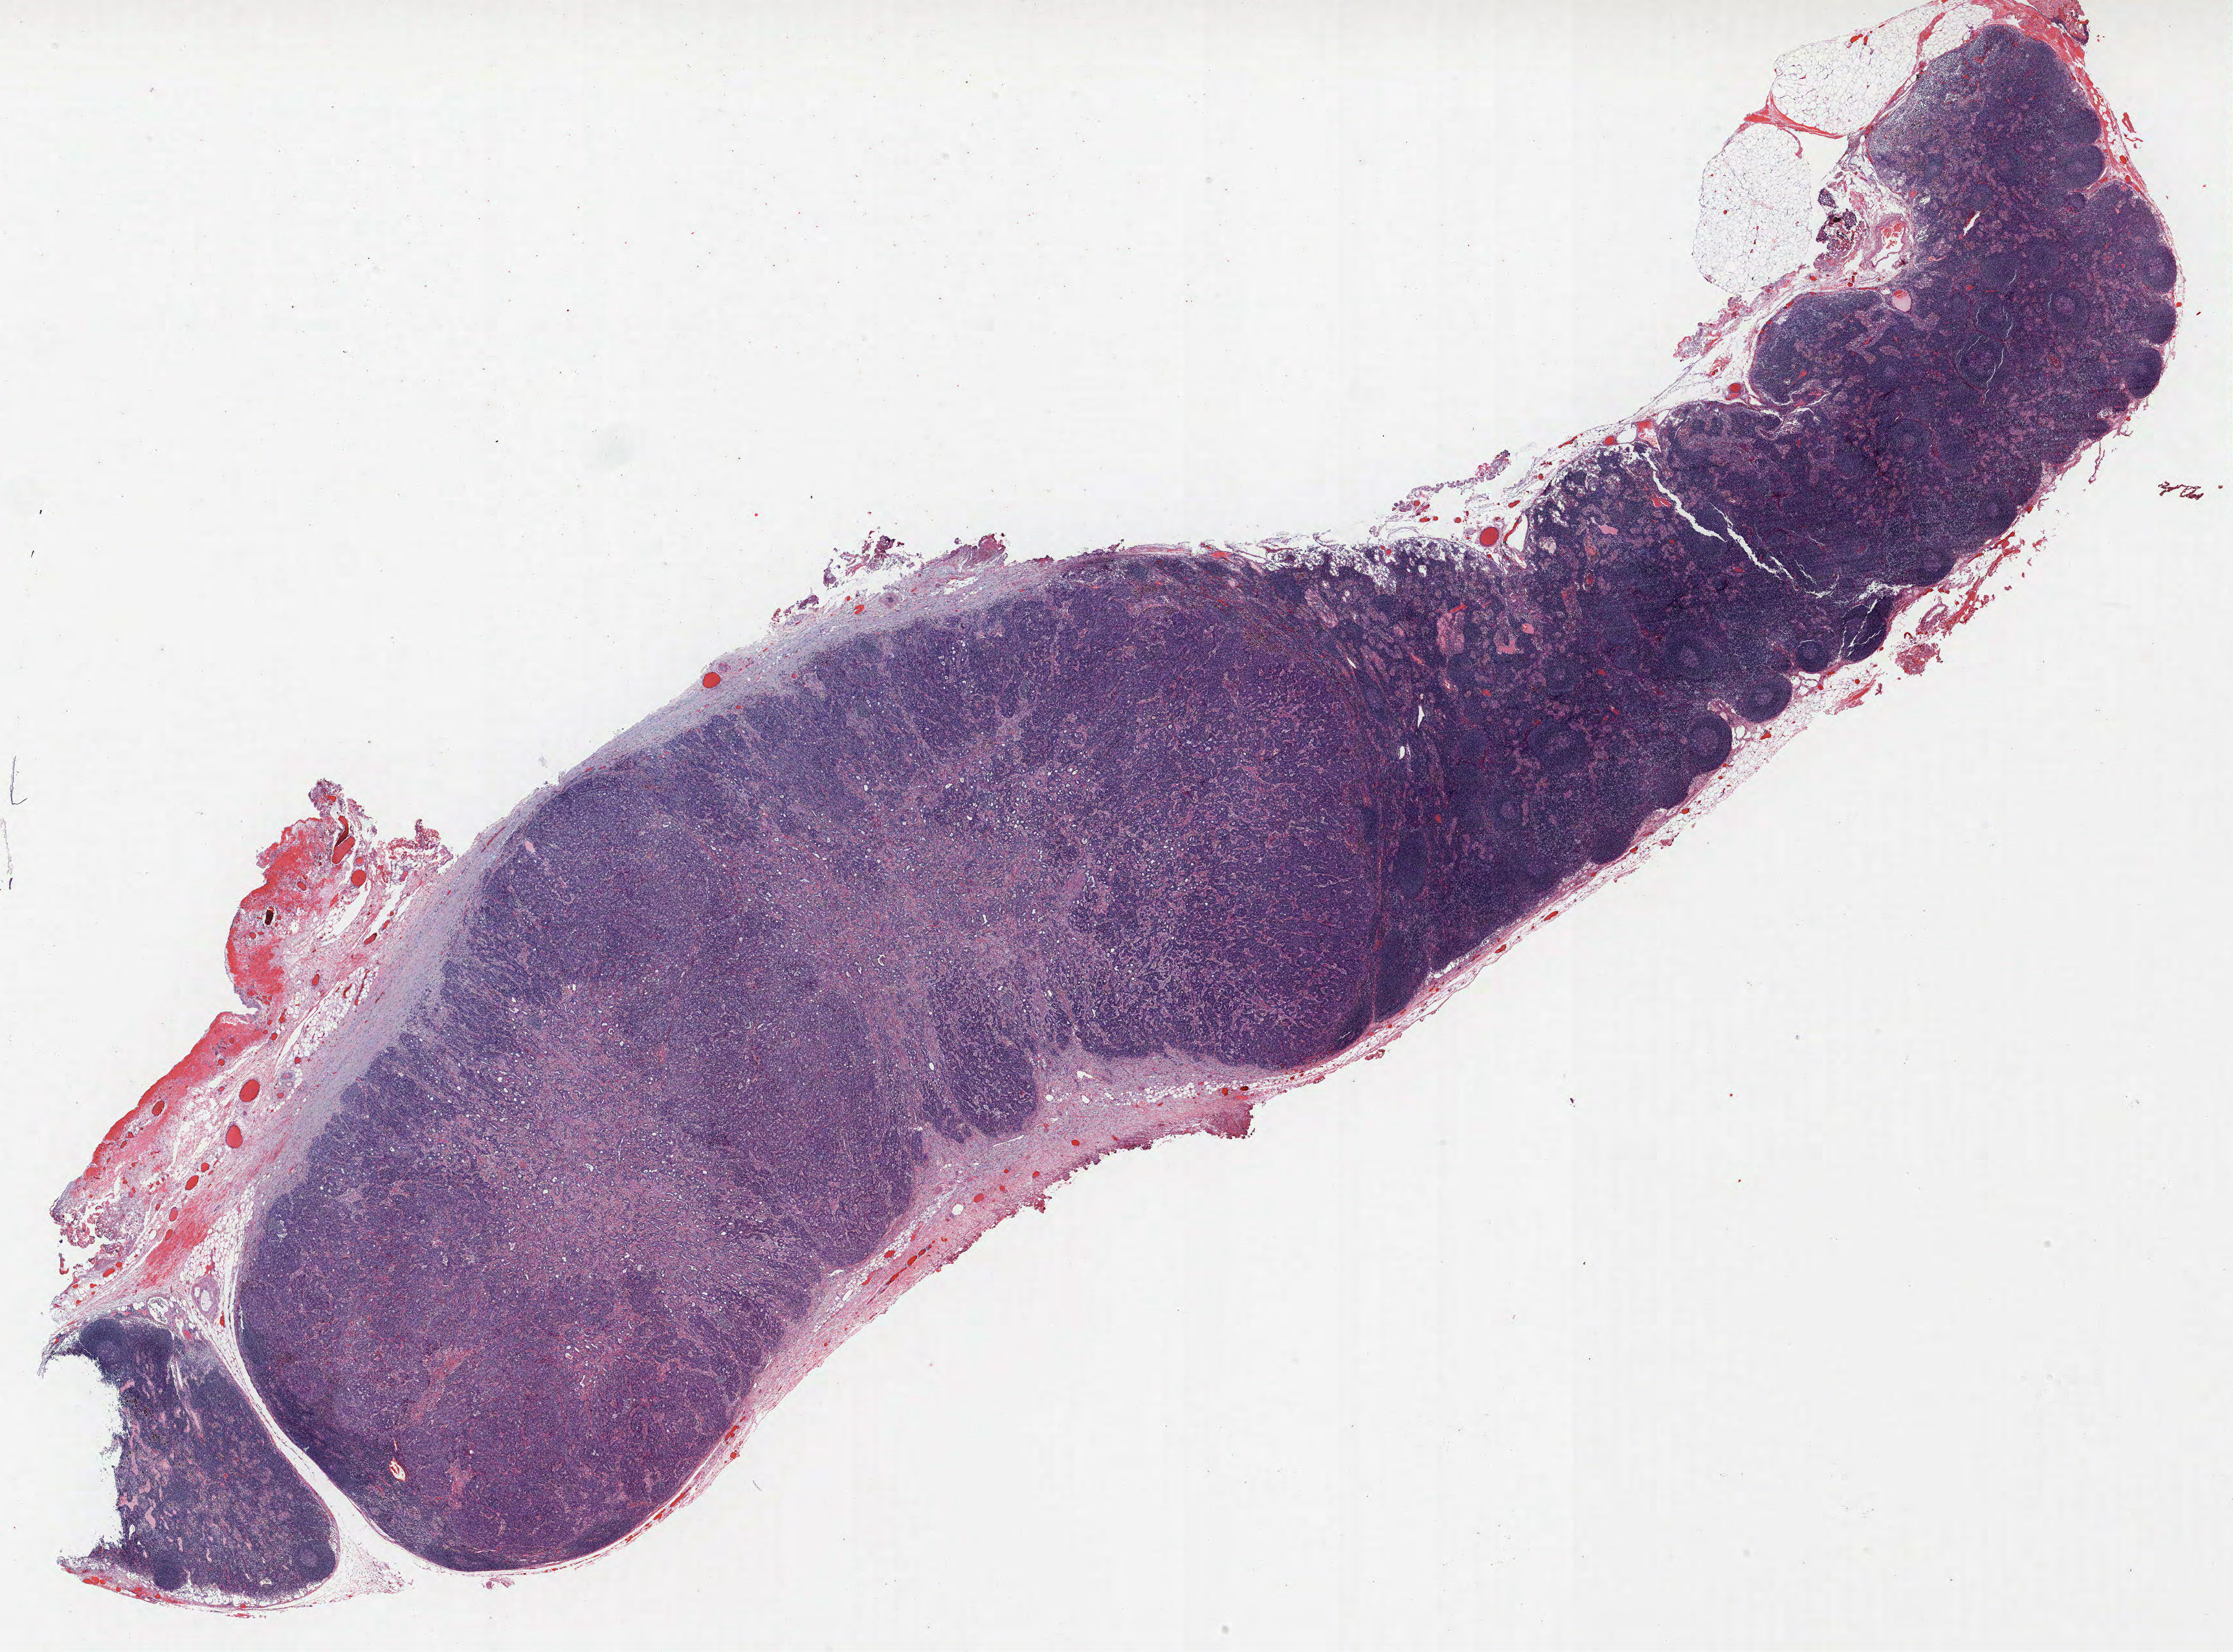
H&E-stained whole-slide image, low-resolution overview of the scanned area, about 27.6 x 20.4 mm (slide scanned at 40x); FFPE section; lung tissue. Female patient, aged 66 at enrolment. Former smoker at enrolment. Grade: moderately differentiated (G2).
* stage (AJCC 6th edition): IV
* primary tumour location (clinical record): right lower lobe
* participant's lung-cancer diagnosis: Adenocarcinoma, NOS (ICD-O-3 8140/3)
* ICD-O-3 topography: lower lobe of lung (C34.3)
* tumour size (pathology): 60 mm